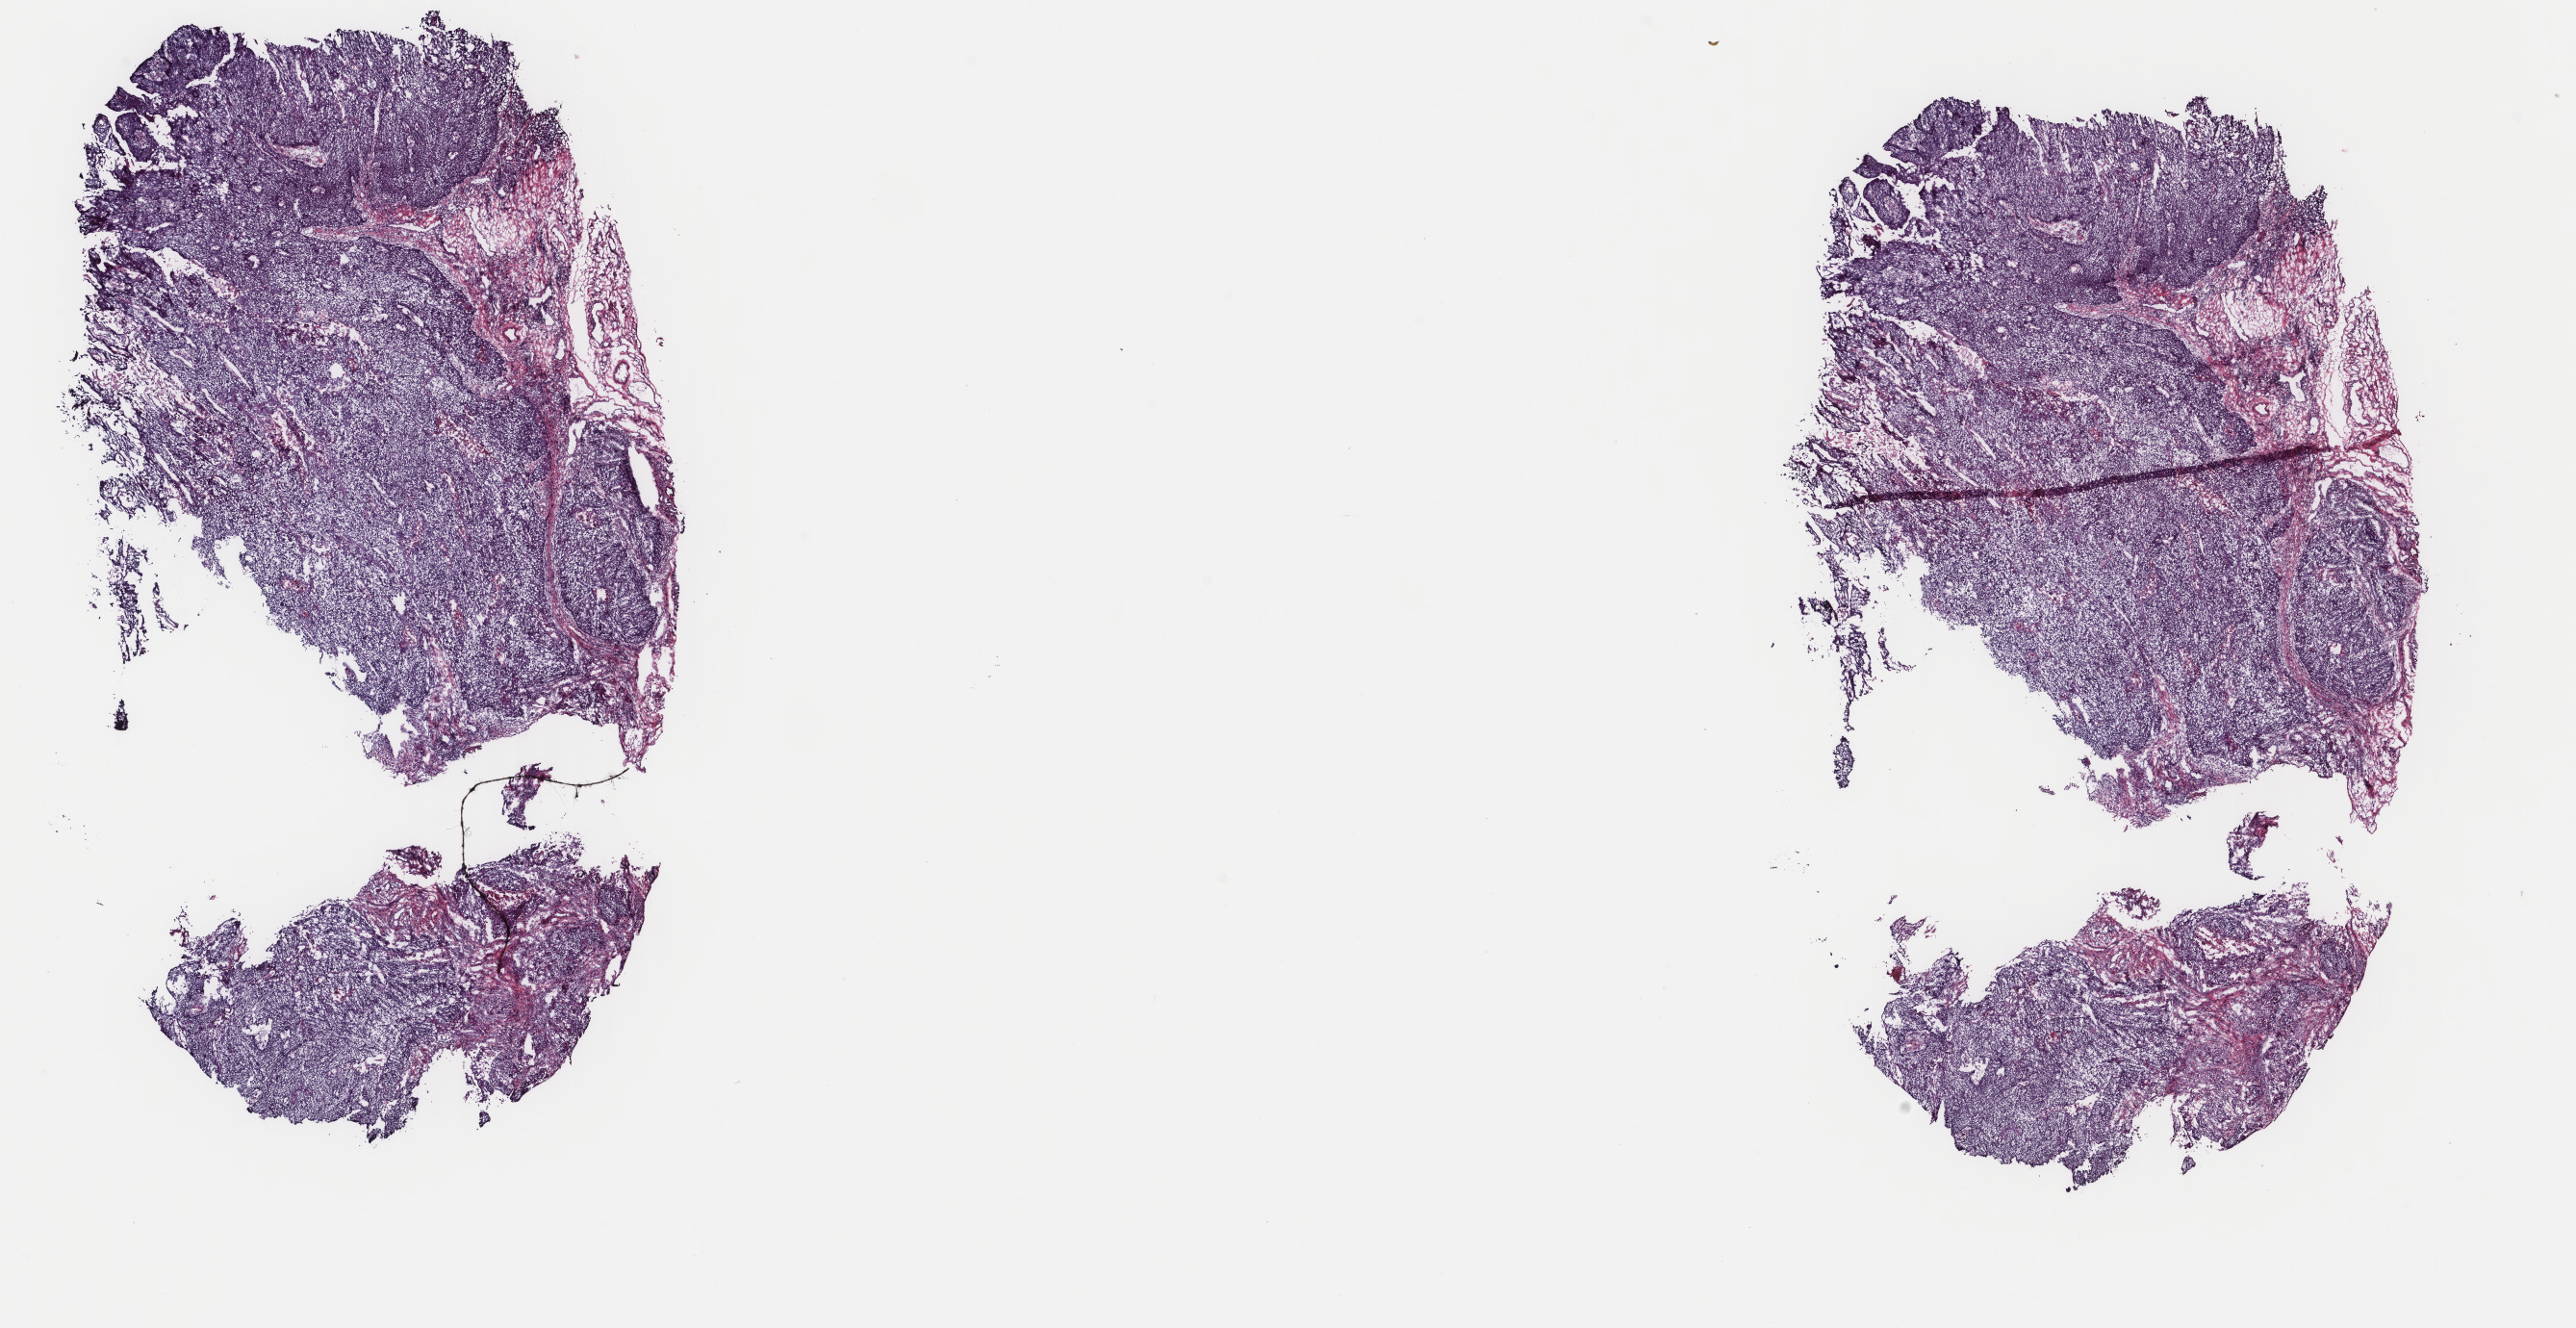
Digitized Hematoxylin and eosin (H&E) stained tissue section (whole slide), a low-resolution overview of the entire scanned area, about 21.2 x 11.0 mm, frozen section from the top of the tissue portion, head and neck, primary tumour sample. Patient: male, age at initial diagnosis 52 years. Histologic grade: GX (grade cannot be assessed). Composition of this section per pathologist review: tumour cells 85%, tumour nuclei 80%, normal cells 13%, stromal cells 0%, necrosis 2%. Infiltration values recorded for this section: lymphocyte infiltration 3%, monocyte infiltration 0%, neutrophil infiltration 0%.
AJCC pathologic stage: III. Diagnosis: Squamous cell carcinoma, NOS (tonsil, NOS).